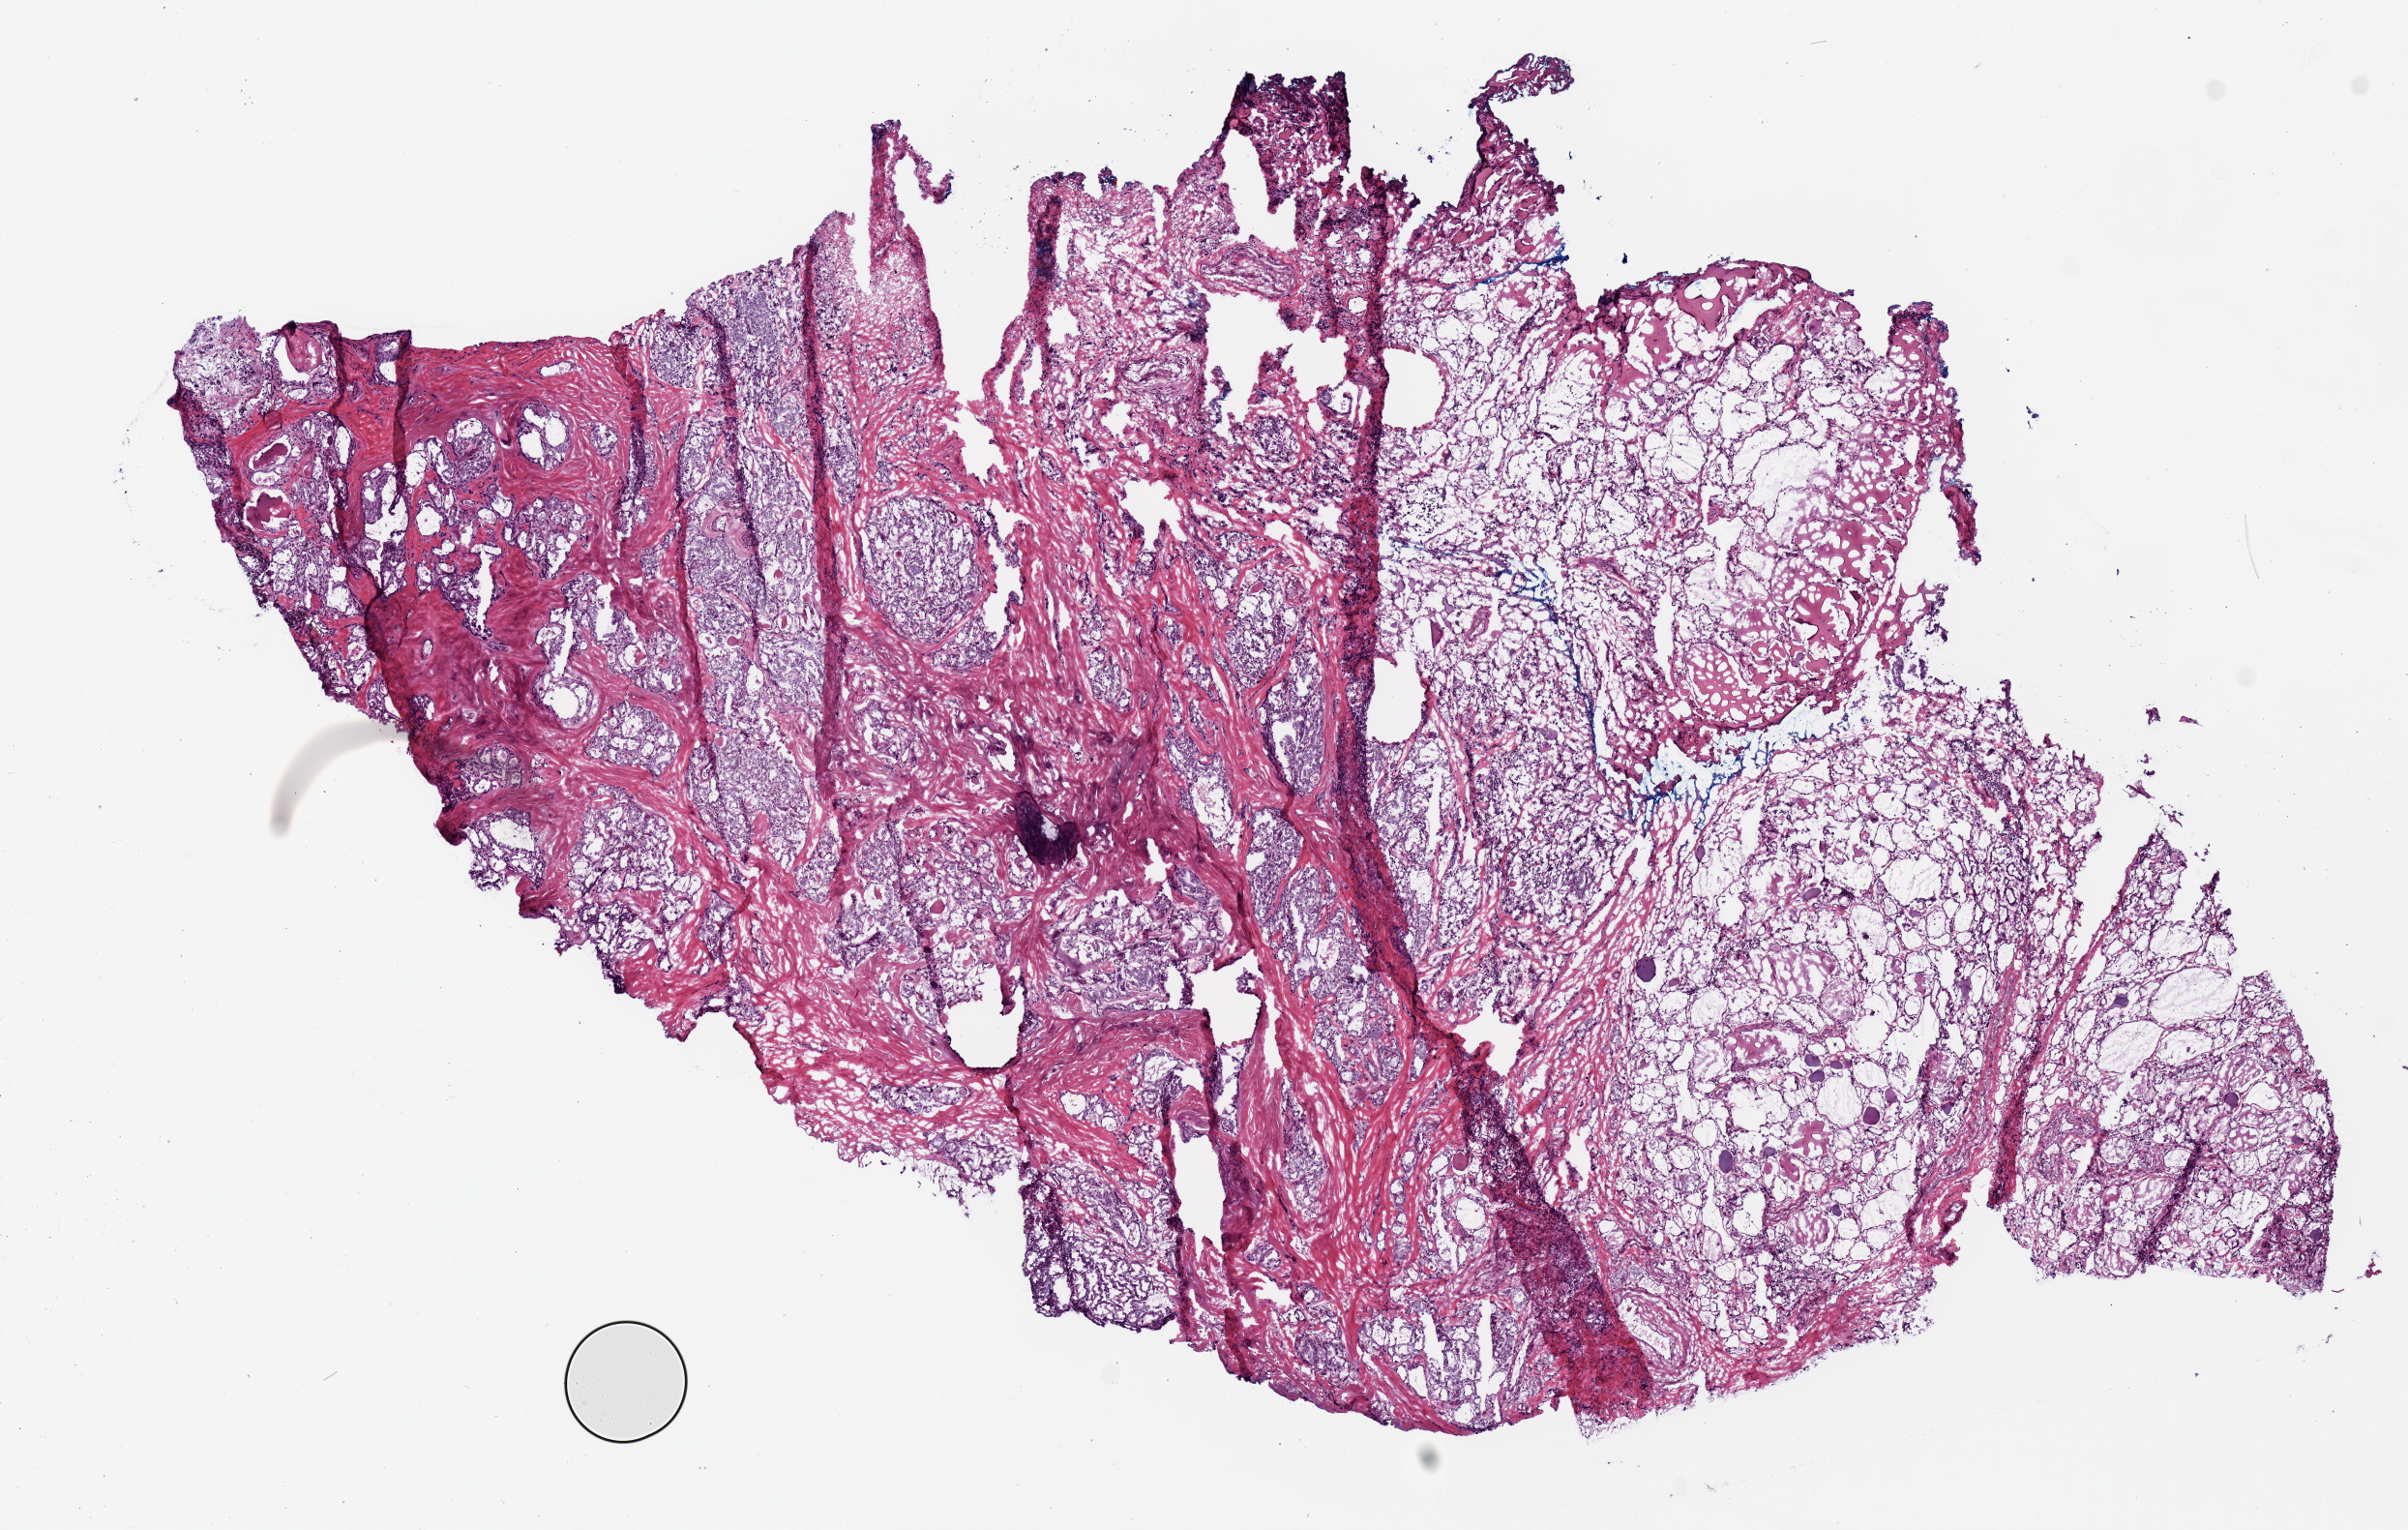
Digitized H&E-stained tissue section (whole slide), a low-resolution overview of the entire scanned area, about 9.8 x 6.2 mm; frozen section; sample: primary tumour, thyroid. Female, age 50 years at initial diagnosis. Slide review estimates, as recorded: tumour cells 100%, tumour nuclei 80%, normal cells 0%, stromal cells 0%, necrosis 0%. Infiltration values recorded for this section: lymphocyte infiltration 2%, monocyte infiltration 0%, neutrophil infiltration 0%.
Histologic diagnosis: Papillary adenocarcinoma, NOS (thyroid gland). AJCC pathologic stage: III (7th edition).